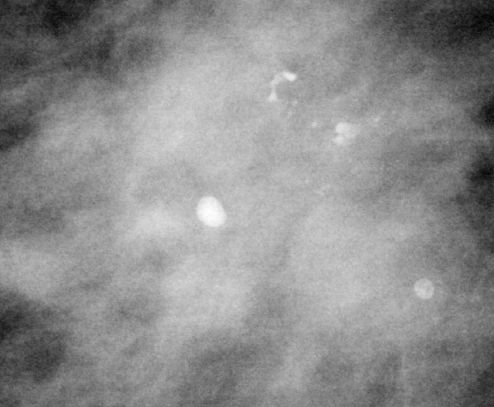
Crop from a digitized film mammogram around one marked abnormality, right breast, MLO view.
- Mass, shape architectural distortion, margins spiculated; BI-RADS assessment category 4; pathology (as recorded): malignant.